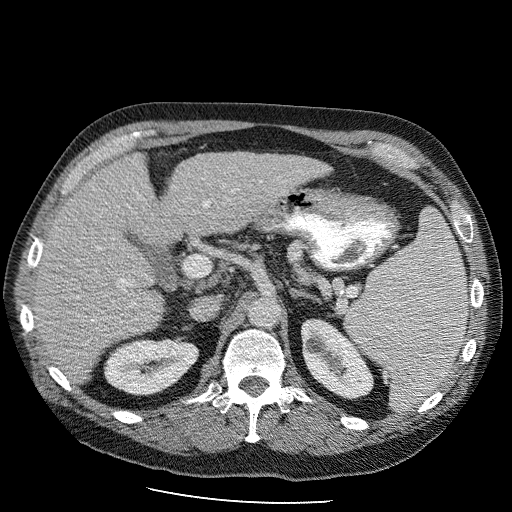
Contrast-enhanced abdominal CT (liver protocol), one axial slice. Slice 54 of 98 in the series (ordered by position). 120 kVp. Soft-tissue window (W 400 / L 40 HU). 2.5 mm slice thickness. 512 × 512 image matrix. Case-level facts recorded for this patient, not image findings: diagnosis: hepatocellular carcinoma (patient treated with transarterial chemoembolisation; whether this scan precedes or follows treatment is not stated here); TNM stage (as recorded): Stage-II; Child-Pugh class: B; tumour nodularity: uninodular.
Structures marked on this image (semi-automatically segmented with operator editing):
- liver parenchyma outside the tumour (the mass and vessels are separate outlines, so this box may not span the whole liver): box from (x=36, y=150) to (x=334, y=380) px
- liver vessels: (x=102, y=195)–(x=211, y=282)